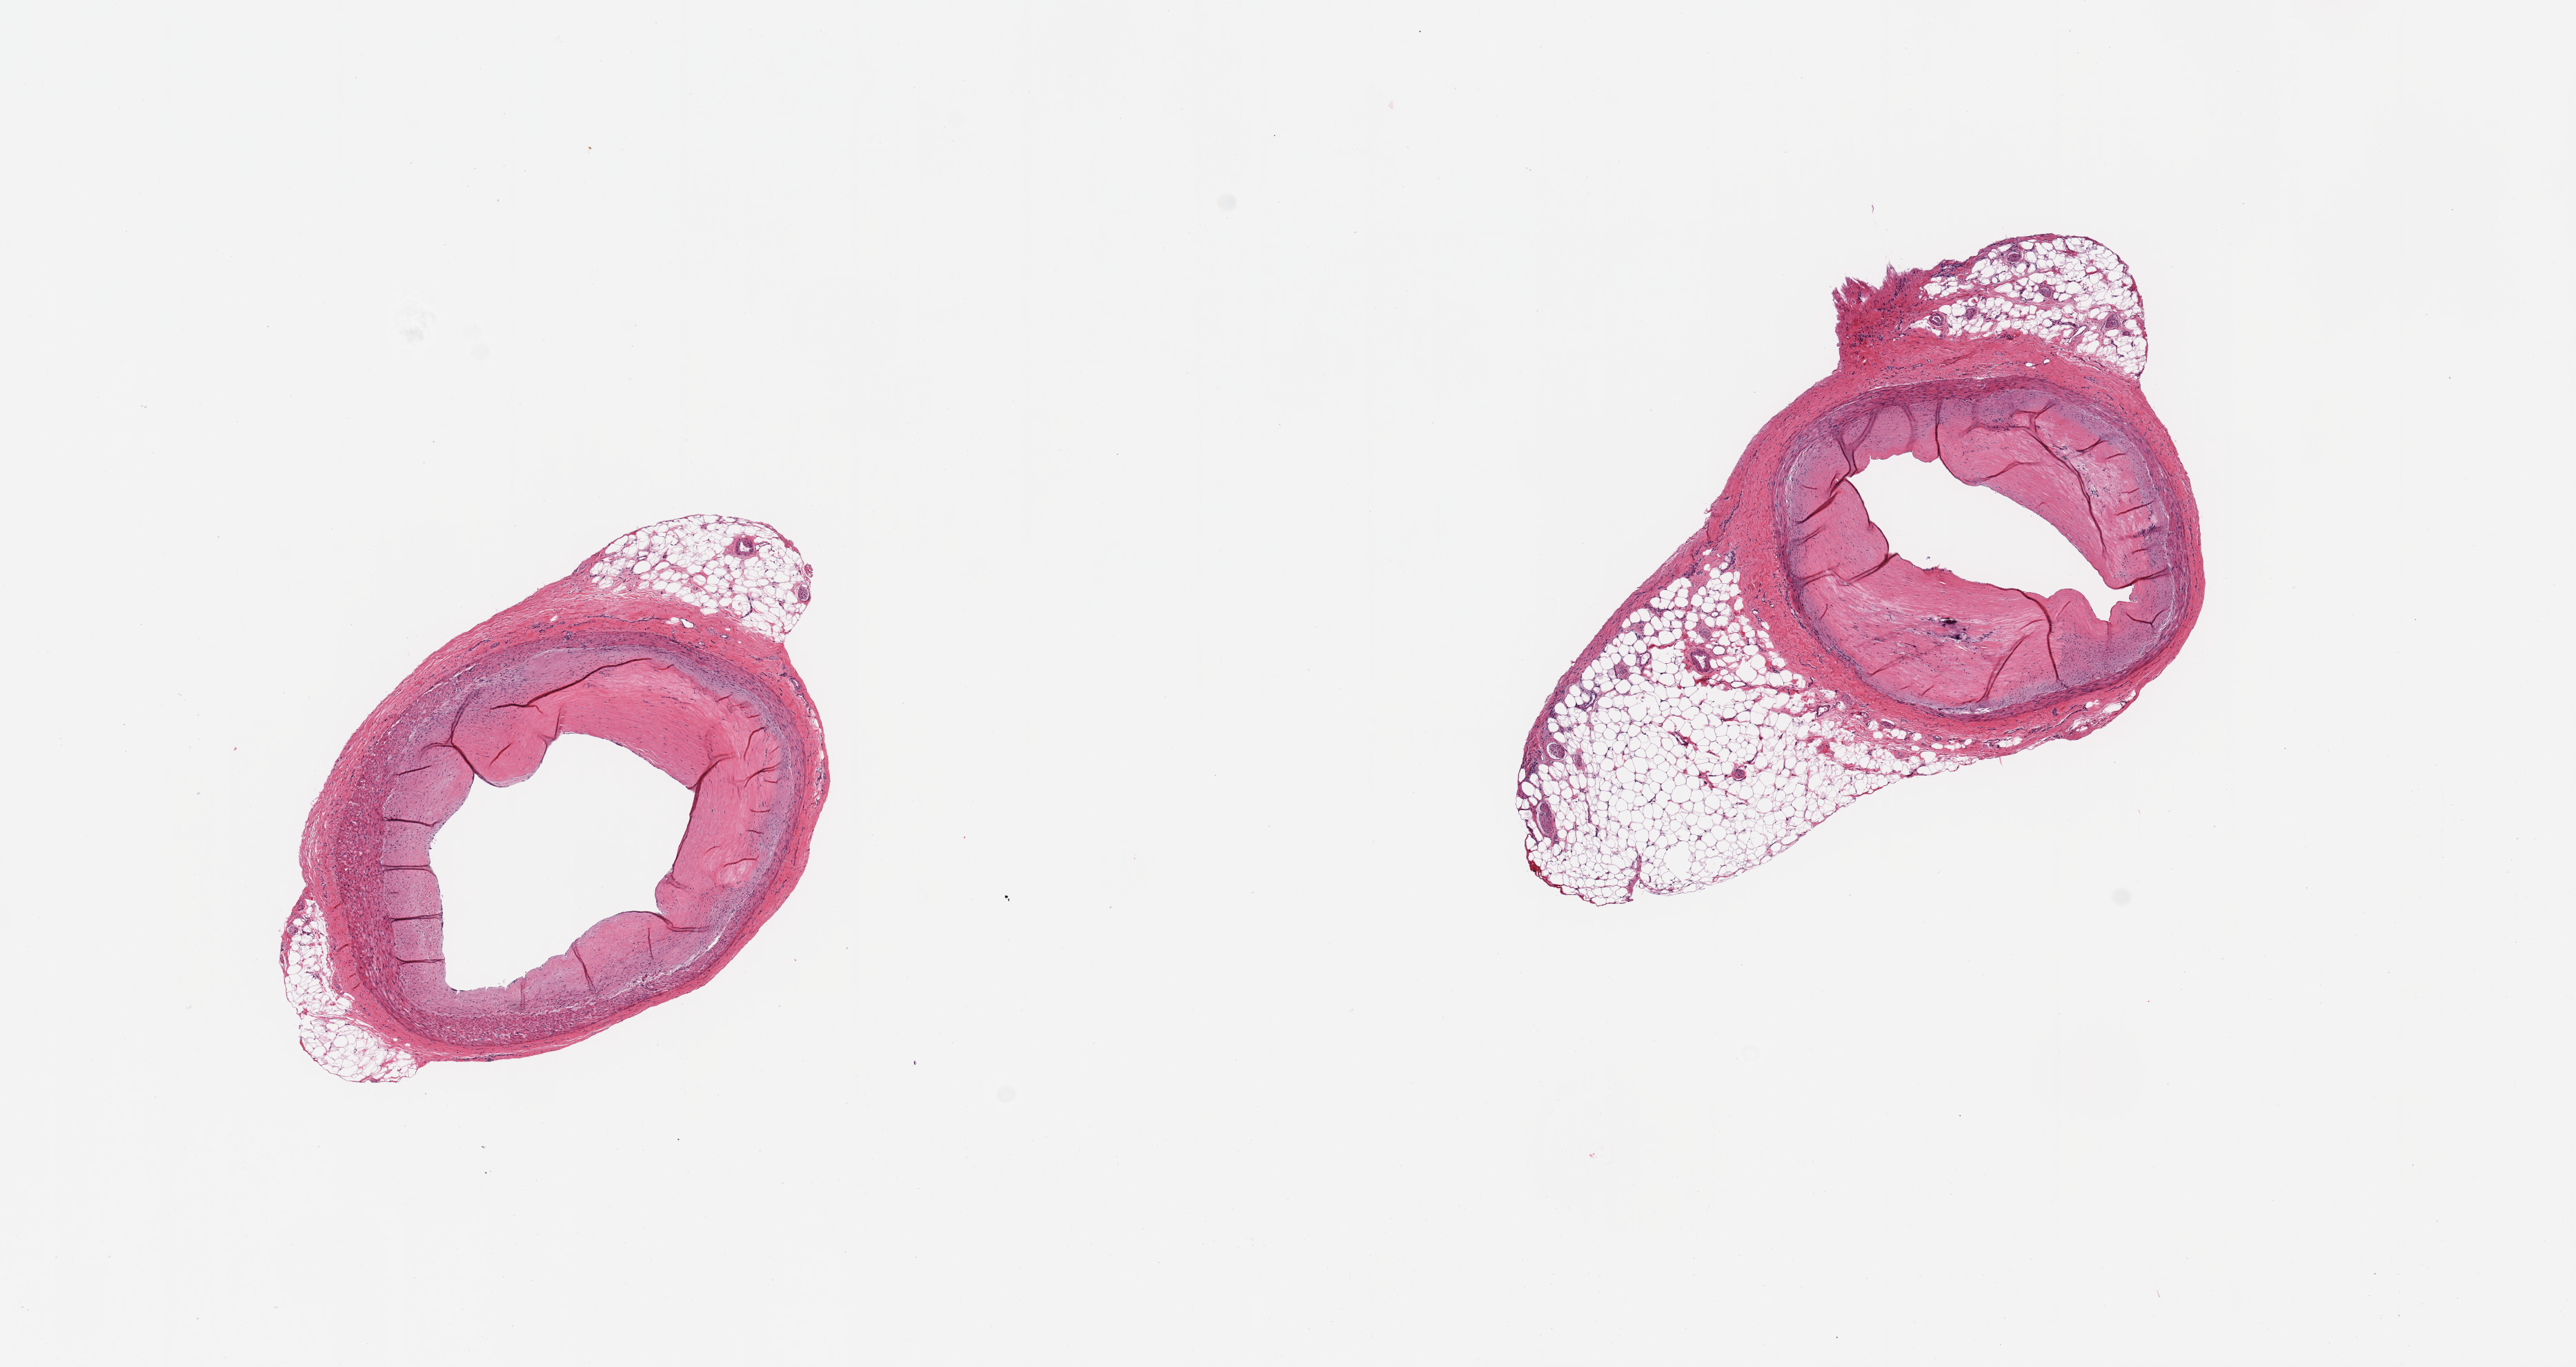
Digitized haematoxylin and eosin-stained section, shown as a low-resolution overview of the whole scanned area (about 14.8 x 7.8 mm, acquisition: 20x scan). PAXgene-fixed, paraffin-embedded tissue. Sampled site (target tissue): coronary artery. Tissue donor sample. Male donor.
Reviewer comment on this tissue sample: 2 pieces; 0.6 up to ~2mm attached fat; atherosclerotic plaque with 50% and 75% luminal compromise and small calcification.